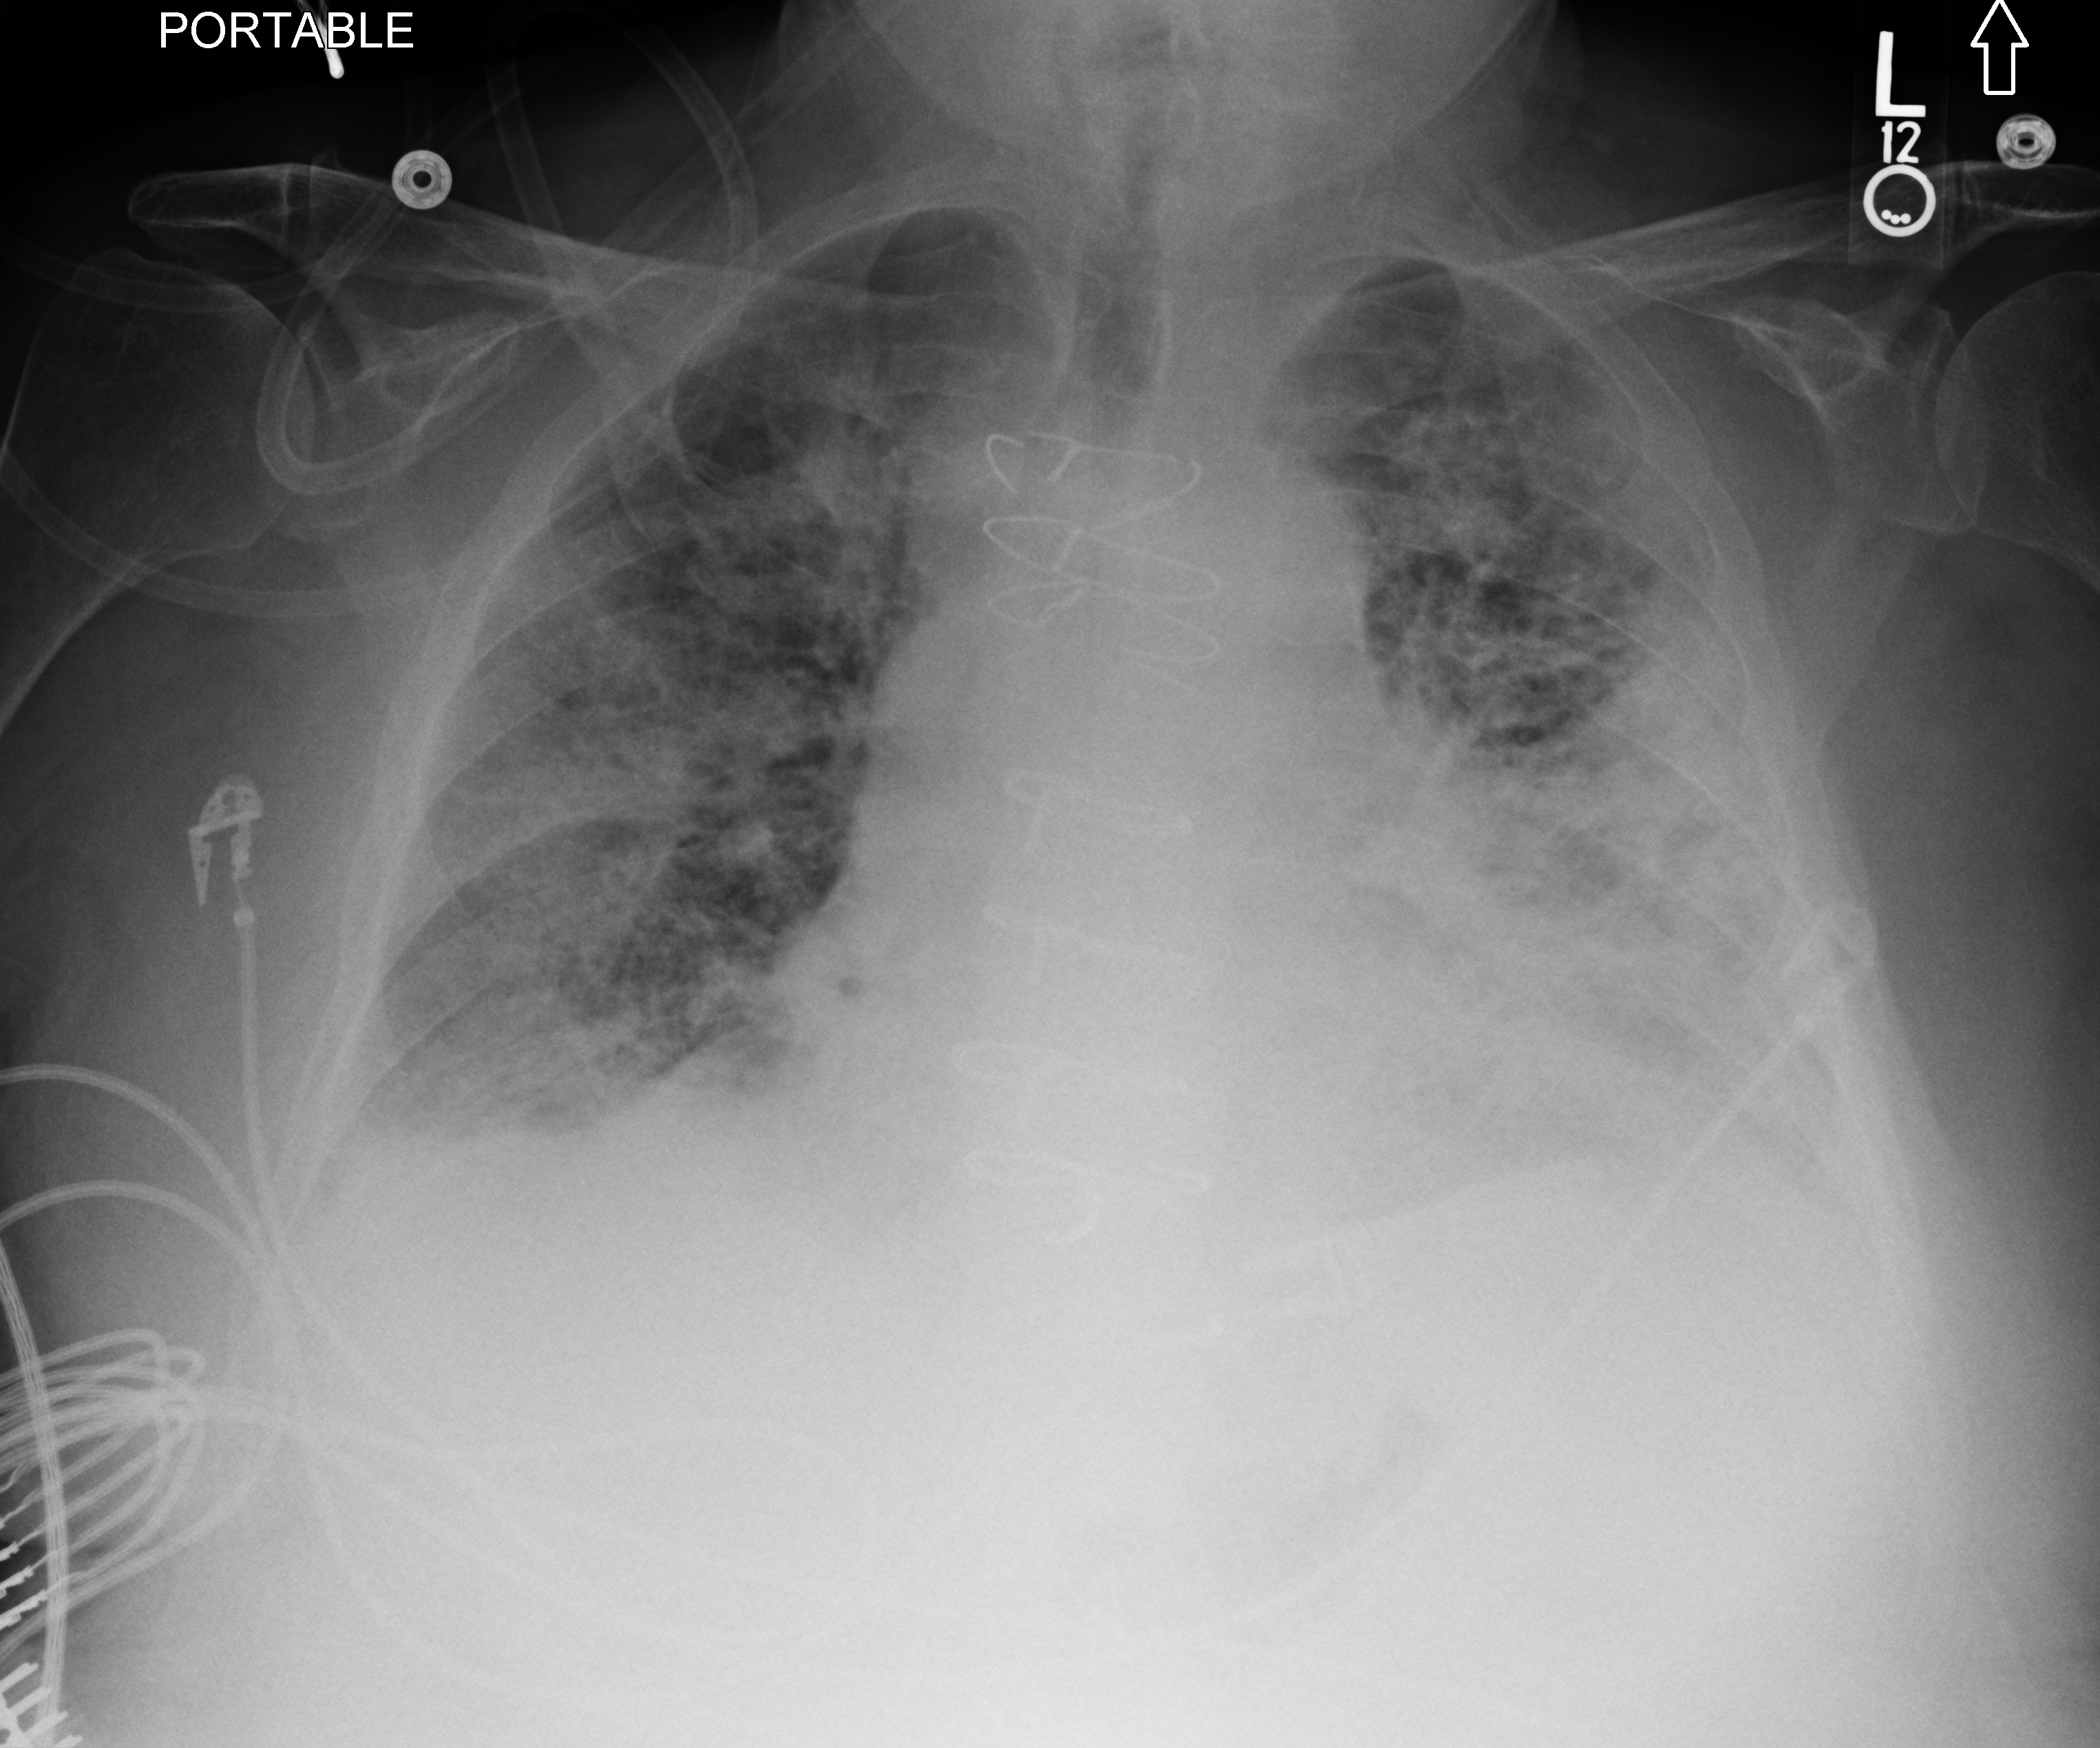
Chest X-ray (portable); anteroposterior (AP) projection. Patient hospitalised with COVID-19; male, aged 75–90 years.
Hospital-stay facts (about this admission, not read from this image; timing relative to this image not recorded):
- diabetes (admission record): yes
- mechanically ventilated during this hospital stay: no
- length of hospital stay: 23 days